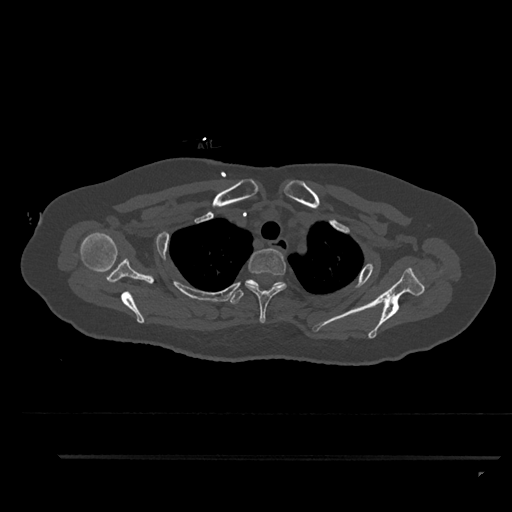
CT including the spine, one axial slice; slice 710 of 797 in the series (ordered by position); reconstruction kernel Br40s/3; 120 kVp; bone window (W 1800 / L 400 HU); 0.5 mm slice thickness; 512 × 512 image matrix. Female patient, age 44 years. Case-level facts recorded for this patient, not image findings: primary cancer: renal.
Outlined on this slice (semi-automatically segmented with operator editing):
- T1 vertebra: bounding box (x1, y1, x2, y2) in pixels: (272, 283, 285, 288)
- T2 vertebra: (245, 248, 287, 323)
- T3 vertebra: (230, 279, 284, 304)